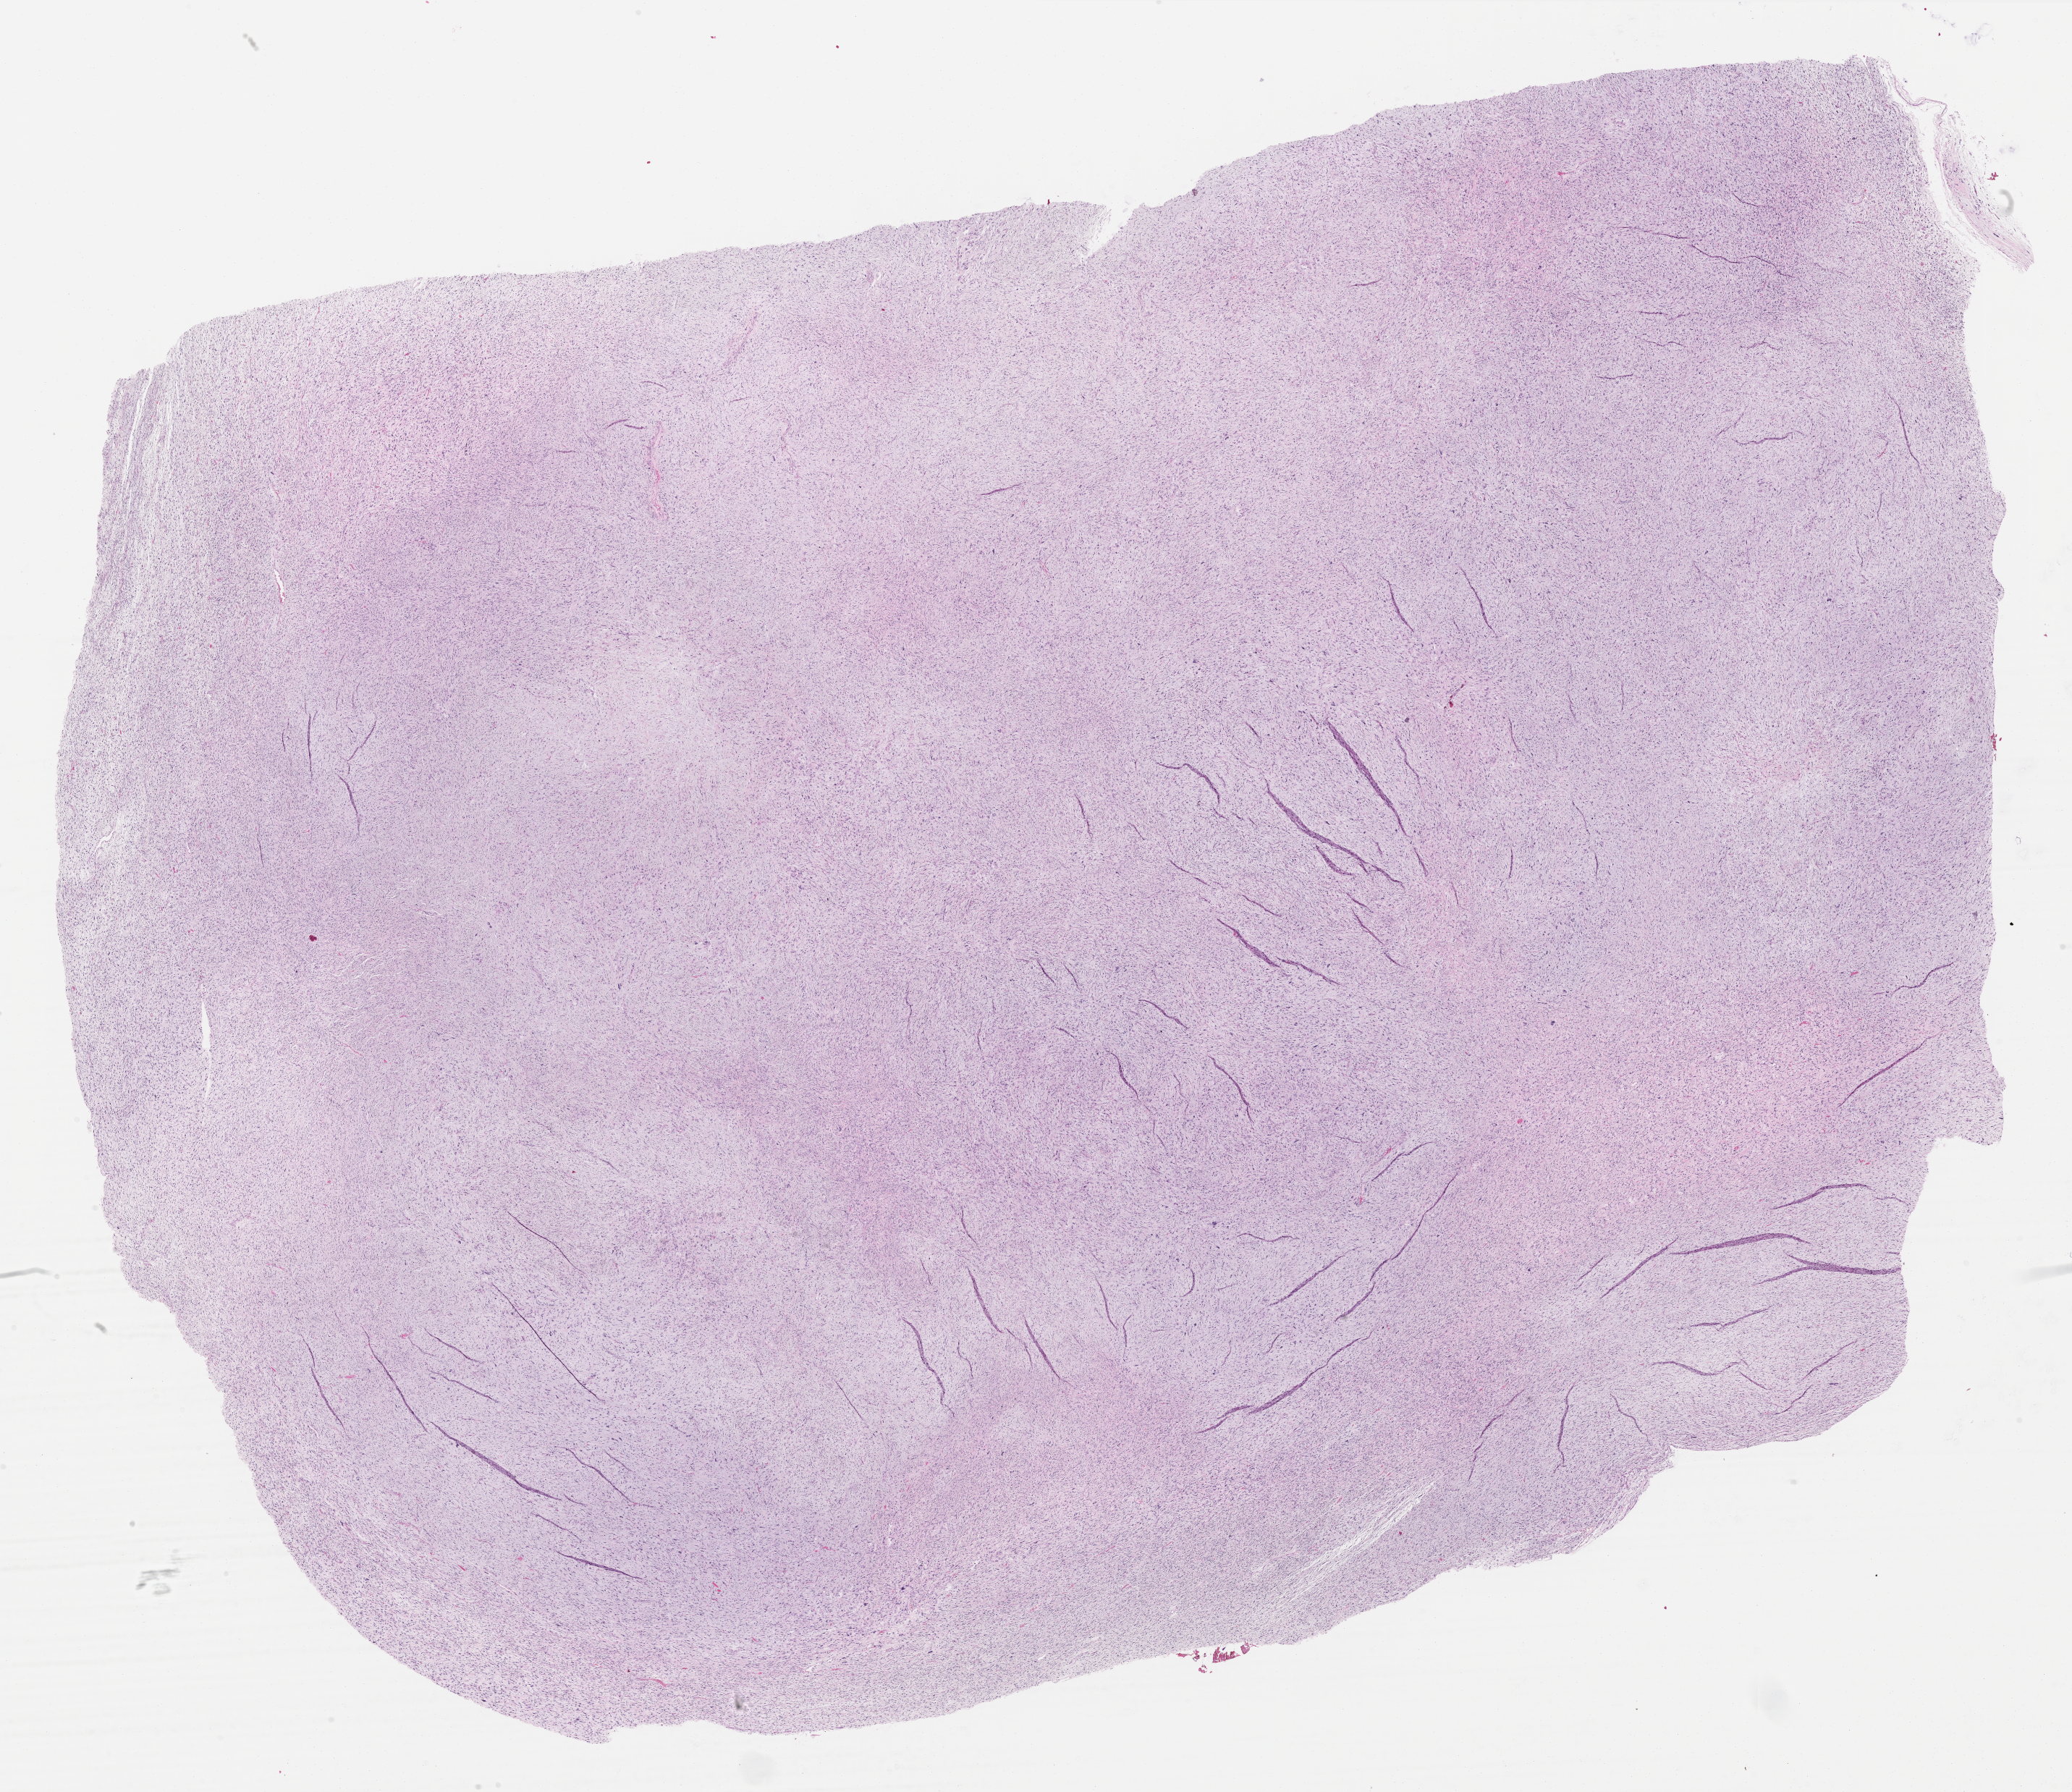
Whole-slide histology image, H&E-stained, whole scanned area (about 23.0 x 19.9 mm) shown as a low-resolution overview, FFPE section, primary tumour sample from the connective, subcutaneous and other soft tissues. Male patient; age at initial diagnosis 75 years.
Pathologic diagnosis: Fibromyxosarcoma.